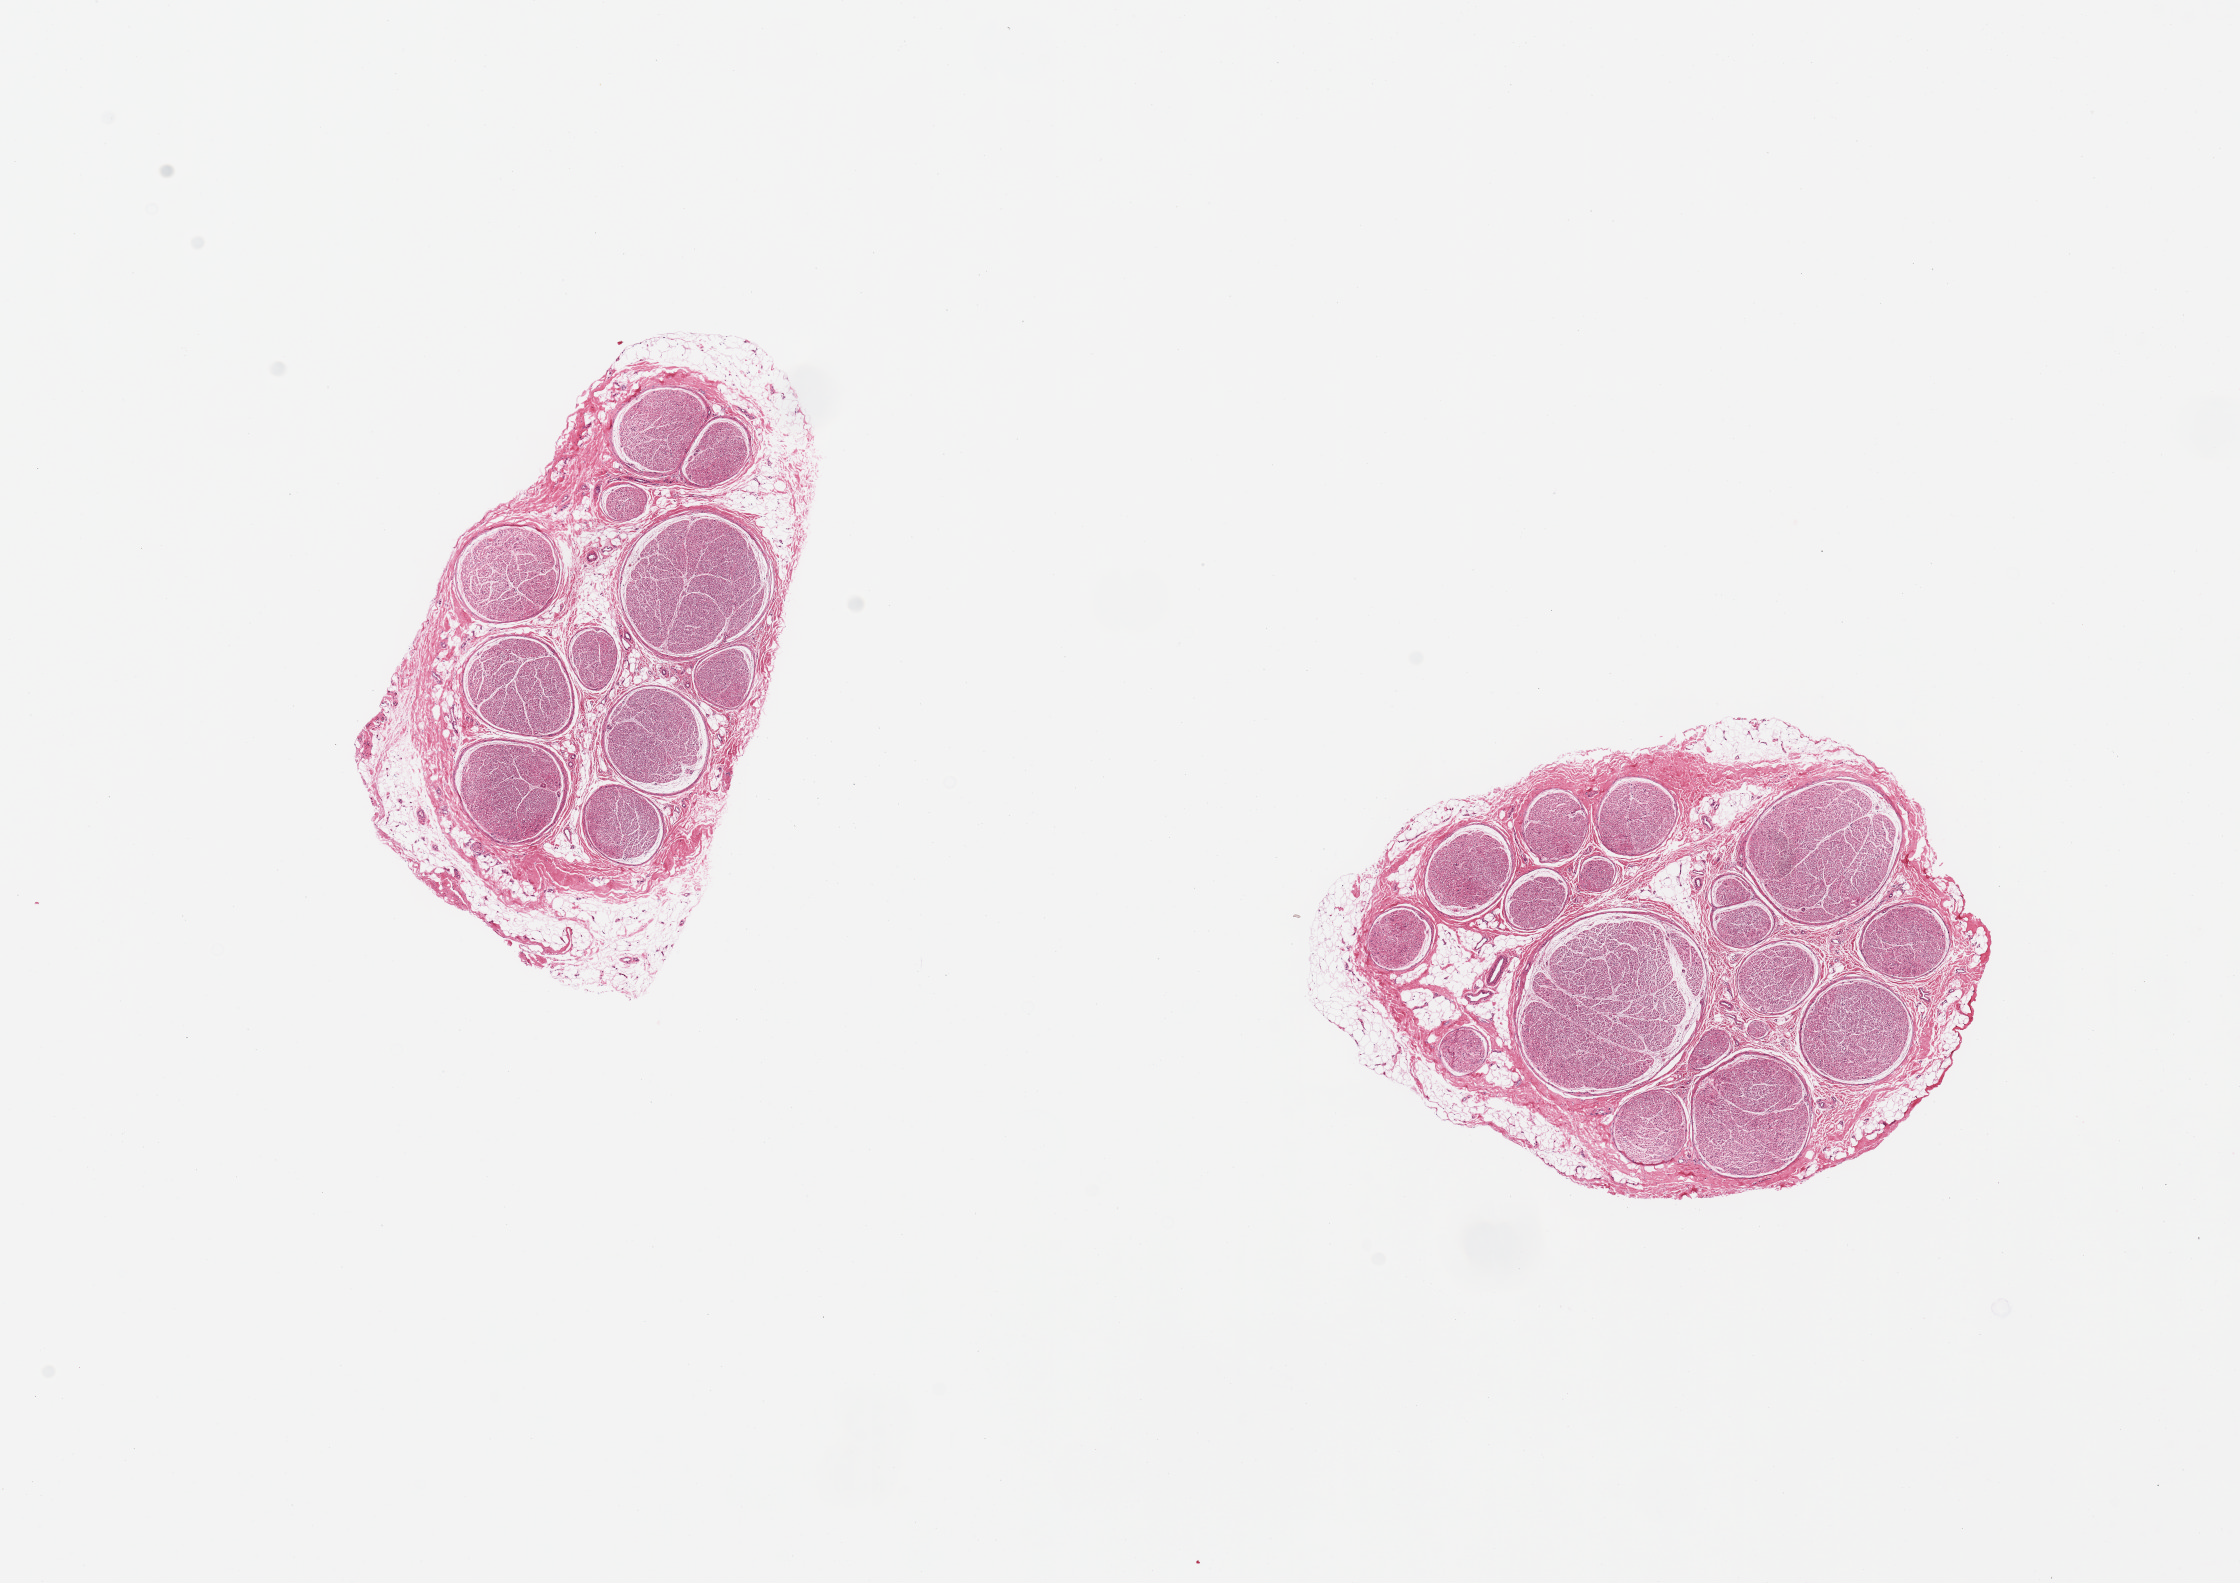
Digitized haematoxylin and eosin-stained section, whole scanned area (about 17.7 x 12.5 mm) shown as a low-resolution overview. PAXgene-fixed paraffin-embedded (PFPE) section. Section of tibial nerve (target tissue). Donor tissue sample. Donor sex: female.
Pathologist's review note for this sample: 2 pieces, attached fat up to 20%.